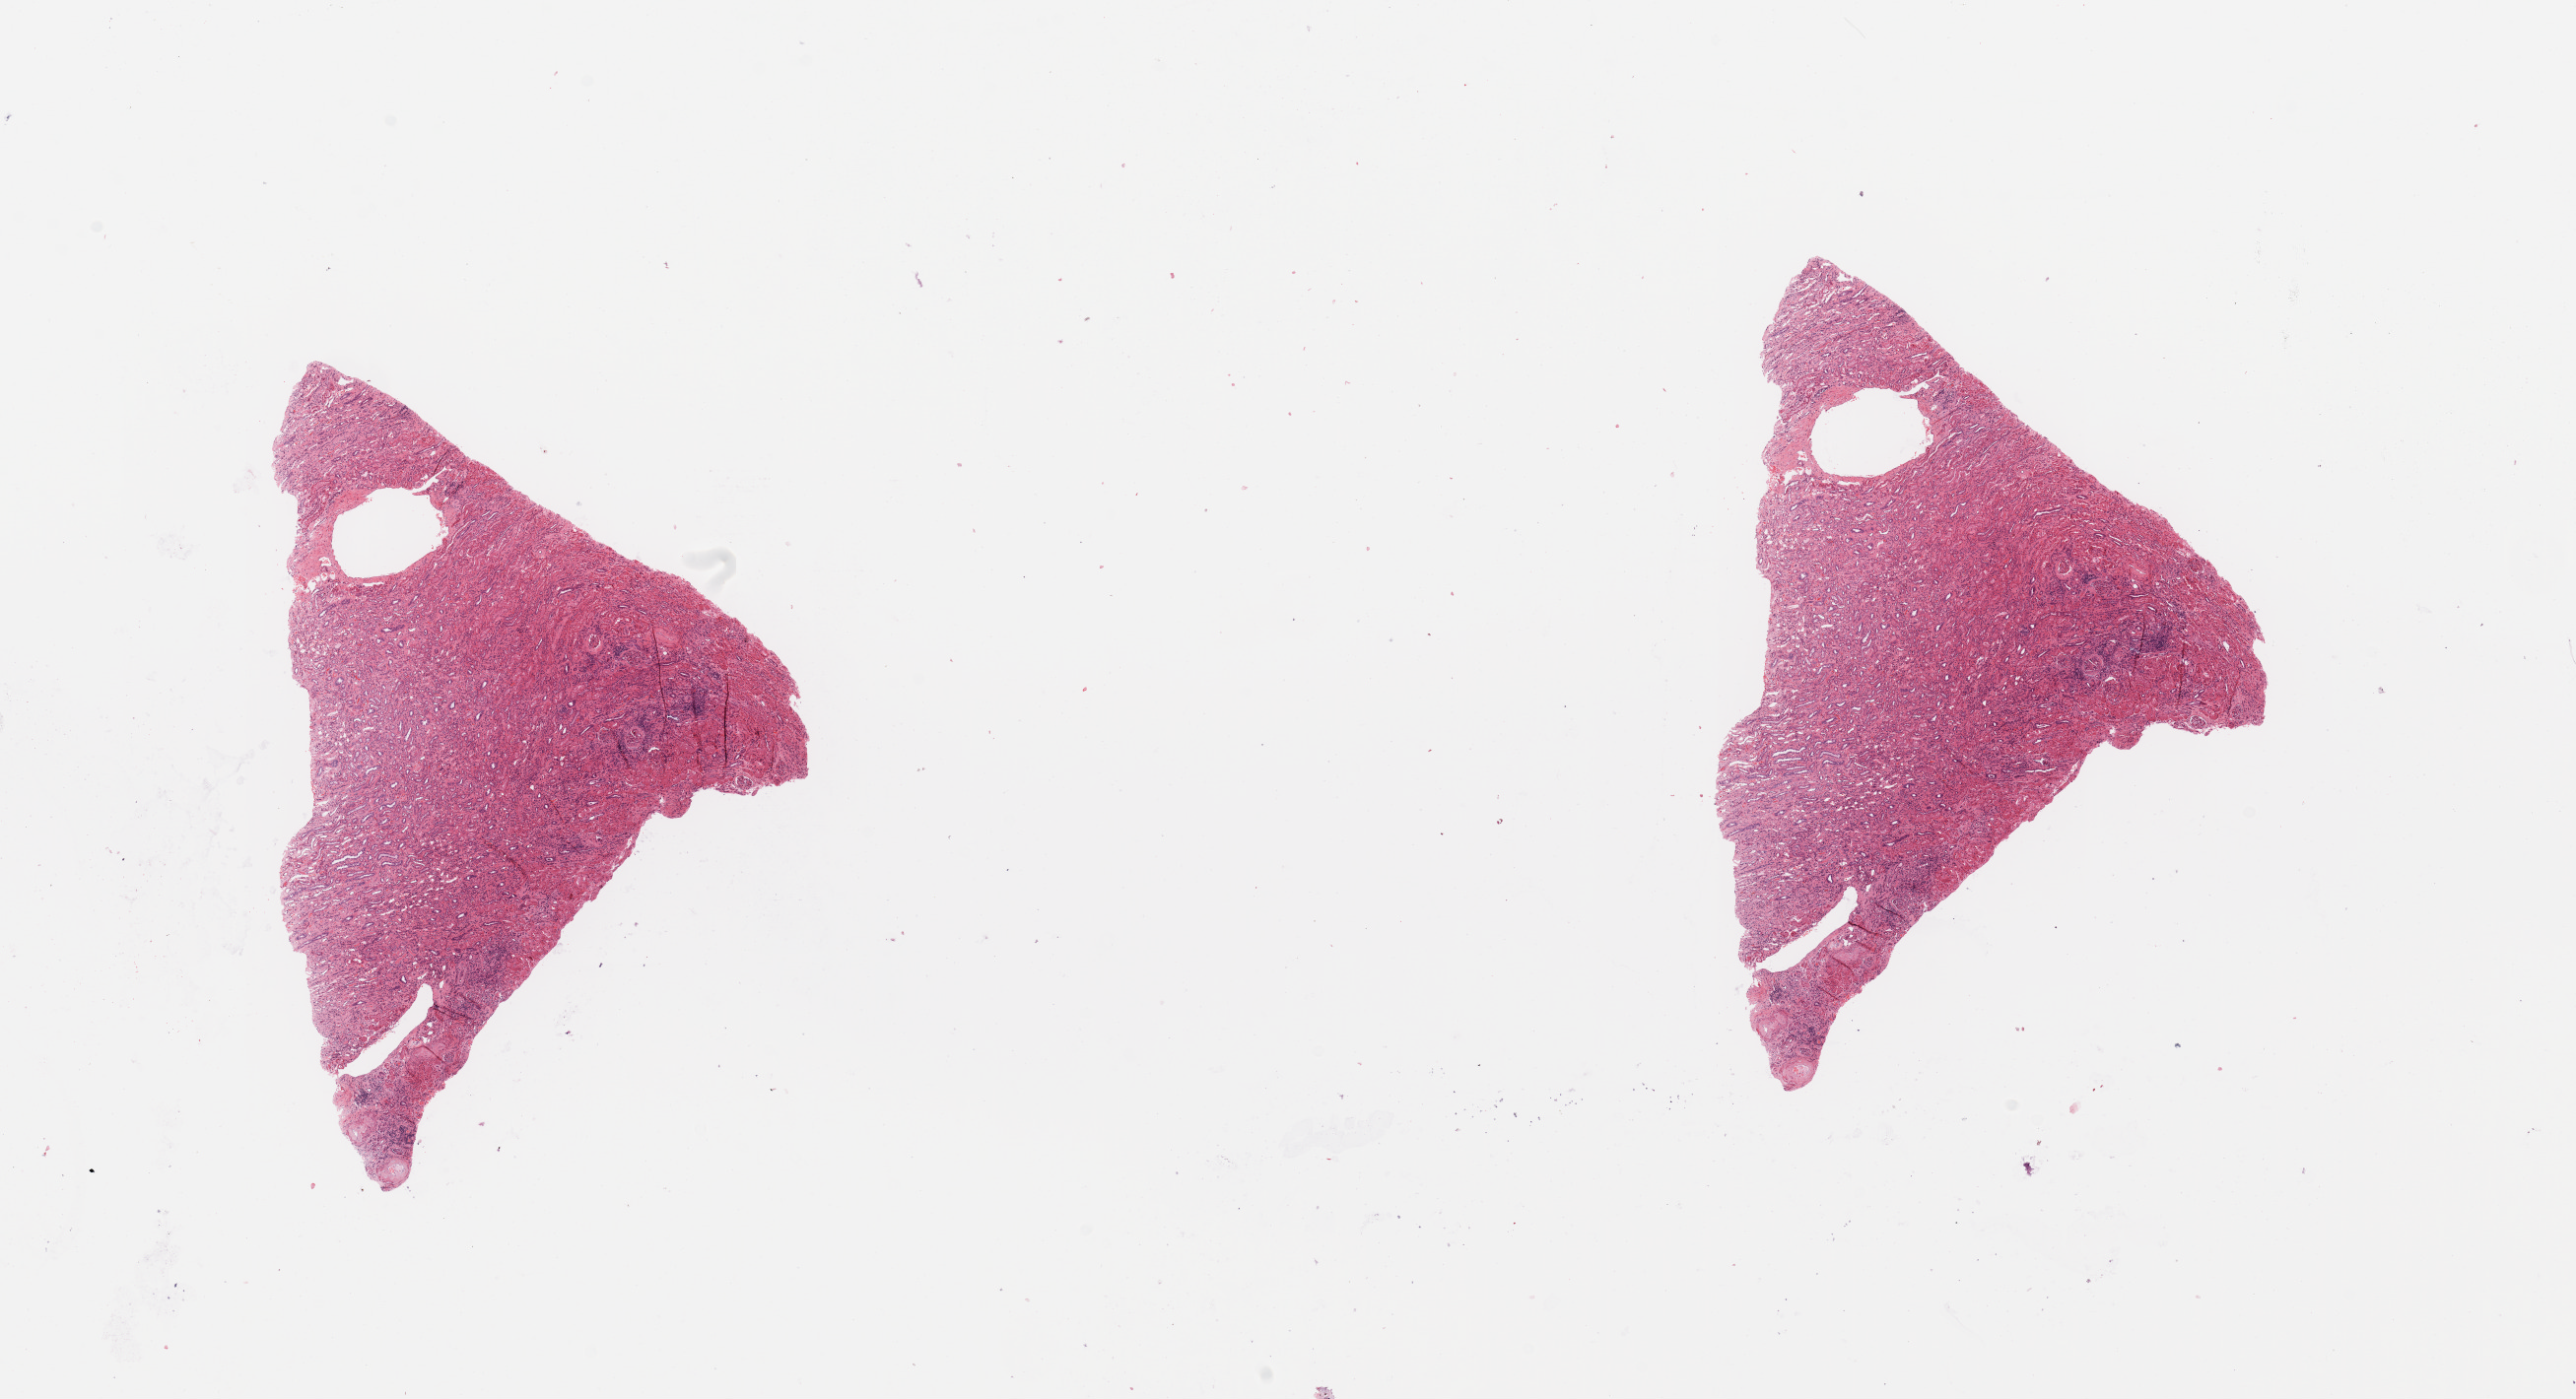
Whole-slide histology image, H&E, shown as a low-resolution overview of the whole scanned area (about 20.7 x 11.2 mm, from a 20x scan). Normal (non-tumour) tissue sample, sampled site: kidney. 54-year-old male patient.
This section: normal (non-tumour) tissue from the same patient. Patient diagnosis: Renal cell carcinoma, NOS.